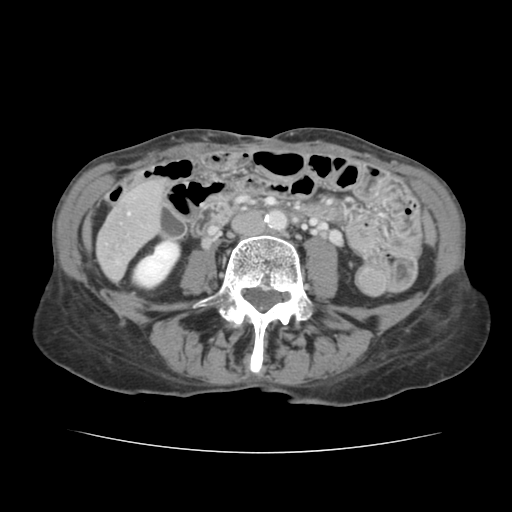
Contrast-enhanced abdominal CT, one axial slice; position 24 of 136 along the scan axis; intravenous contrast given; soft-tissue window (W 400 / L 40 HU); 2.5 mm slice thickness; 512 × 512 image matrix, field of view 319 × 319 mm. Female patient, age 77 years. Case-level facts recorded for this patient, not image findings: diagnosis: colorectal cancer liver metastases, imaged before liver resection; multiple liver metastases: yes; largest metastasis: 3 cm; disease in both lobes: no.
Annotated regions visible in this slice (outlined manually by an expert reader):
- liver: bounding box <98,183,162,279> (left, top, right, bottom; pixels)